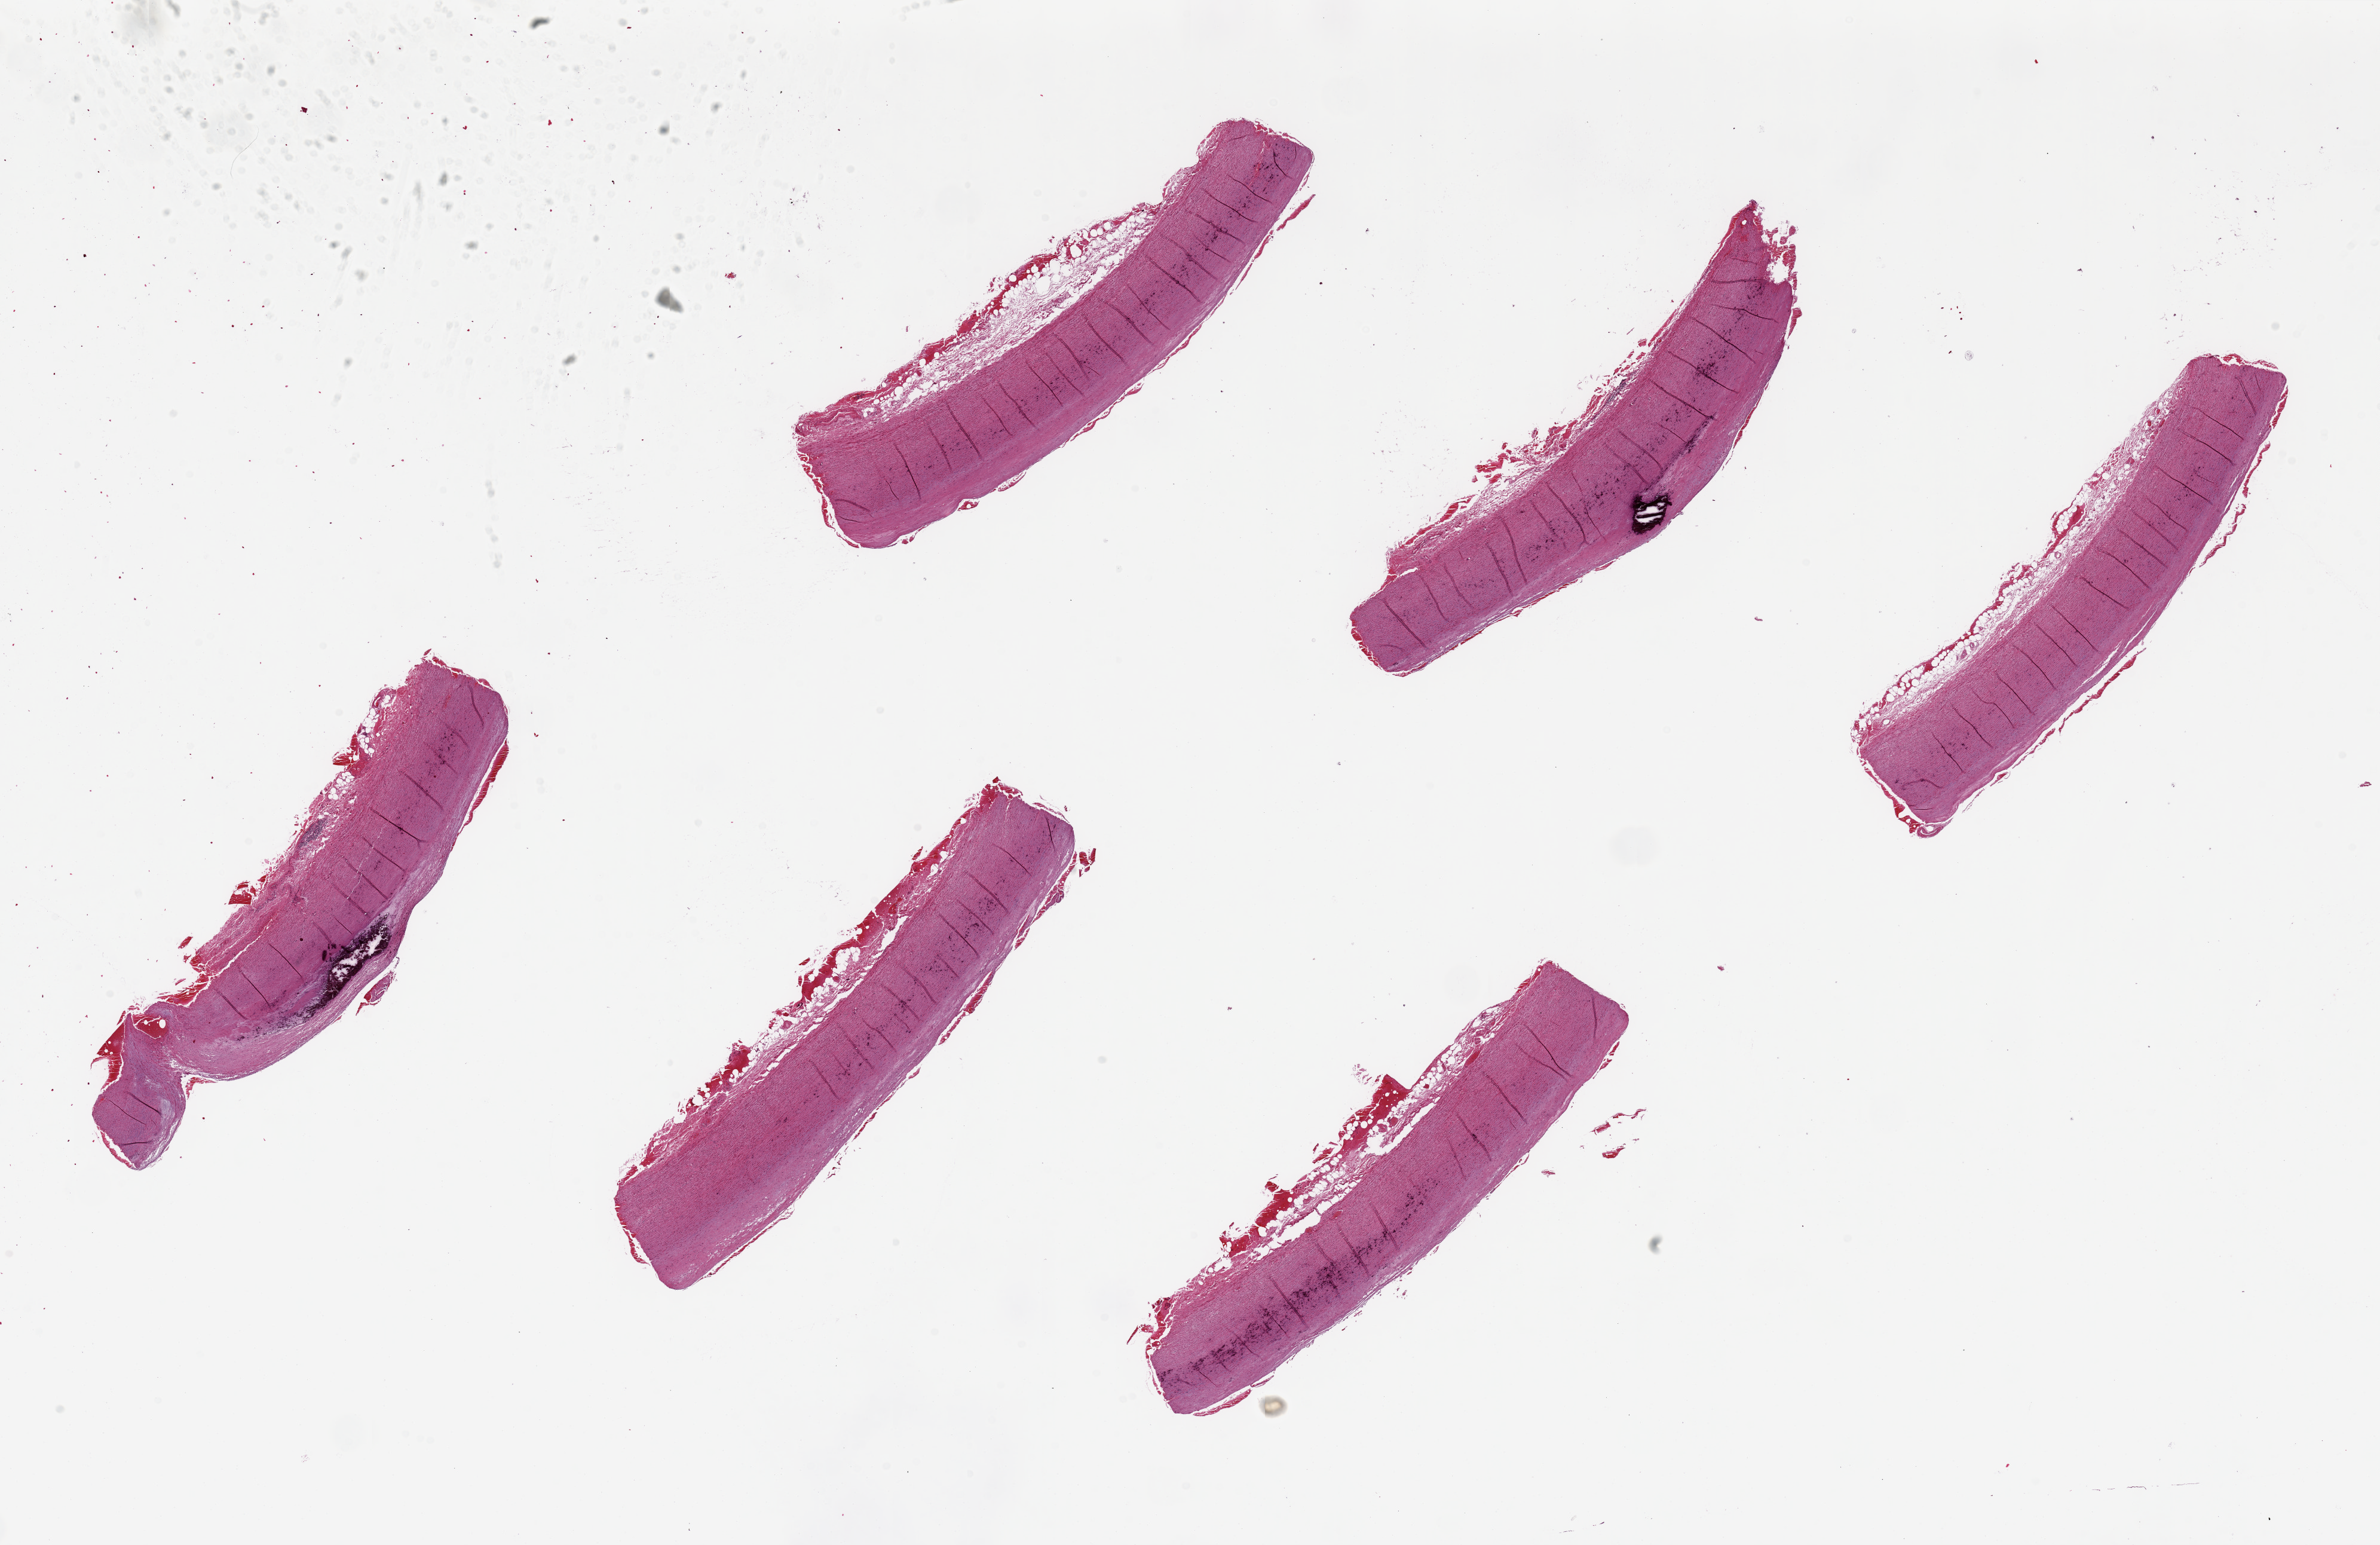
Whole-slide image, H&E stain, brightfield — low-resolution overview of the scanned area, about 31.5 x 20.4 mm (acquisition: 20x scan). PAXgene-fixed, paraffin-embedded tissue. Sampled site (target tissue): aorta. Tissue donor sample. Donor sex: female.
• review note (as recorded): 6 pieces, up to 8x2mm; up to ~0.5mm adherent atherosis, calcified focally, also ~0.5mm serosal/advential fat